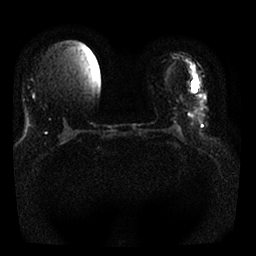
Breast MRI, one axial slice. Slice 9 of 25 in the series (ordered by position). Diffusion-weighted series; image 2 of 4 stored at this slice position (different b-values; order by instance number). 1.5 T. 256 × 256 image matrix, field of view 320 × 320 mm. Female patient.
Annotated regions visible in this slice (outlined manually by an expert reader):
- tumour on diffusion-weighted imaging: bounding box (x1, y1, x2, y2) in pixels: (193, 82, 197, 92)